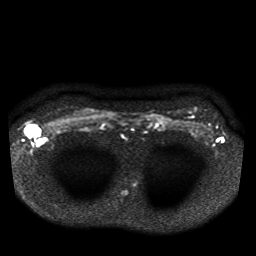
Breast MRI, one axial slice. Slice 33 of 41 in the series (ordered by position). Diffusion-weighted series; image 2 of 4 stored at this slice position (different b-values; order by instance number). 1.5 T. 256 × 256 image matrix, field of view 330 × 330 mm. Female patient.
Outlined on this slice (manually delineated by an expert):
- tumour on diffusion-weighted imaging: box from (x=25, y=125) to (x=35, y=136) px